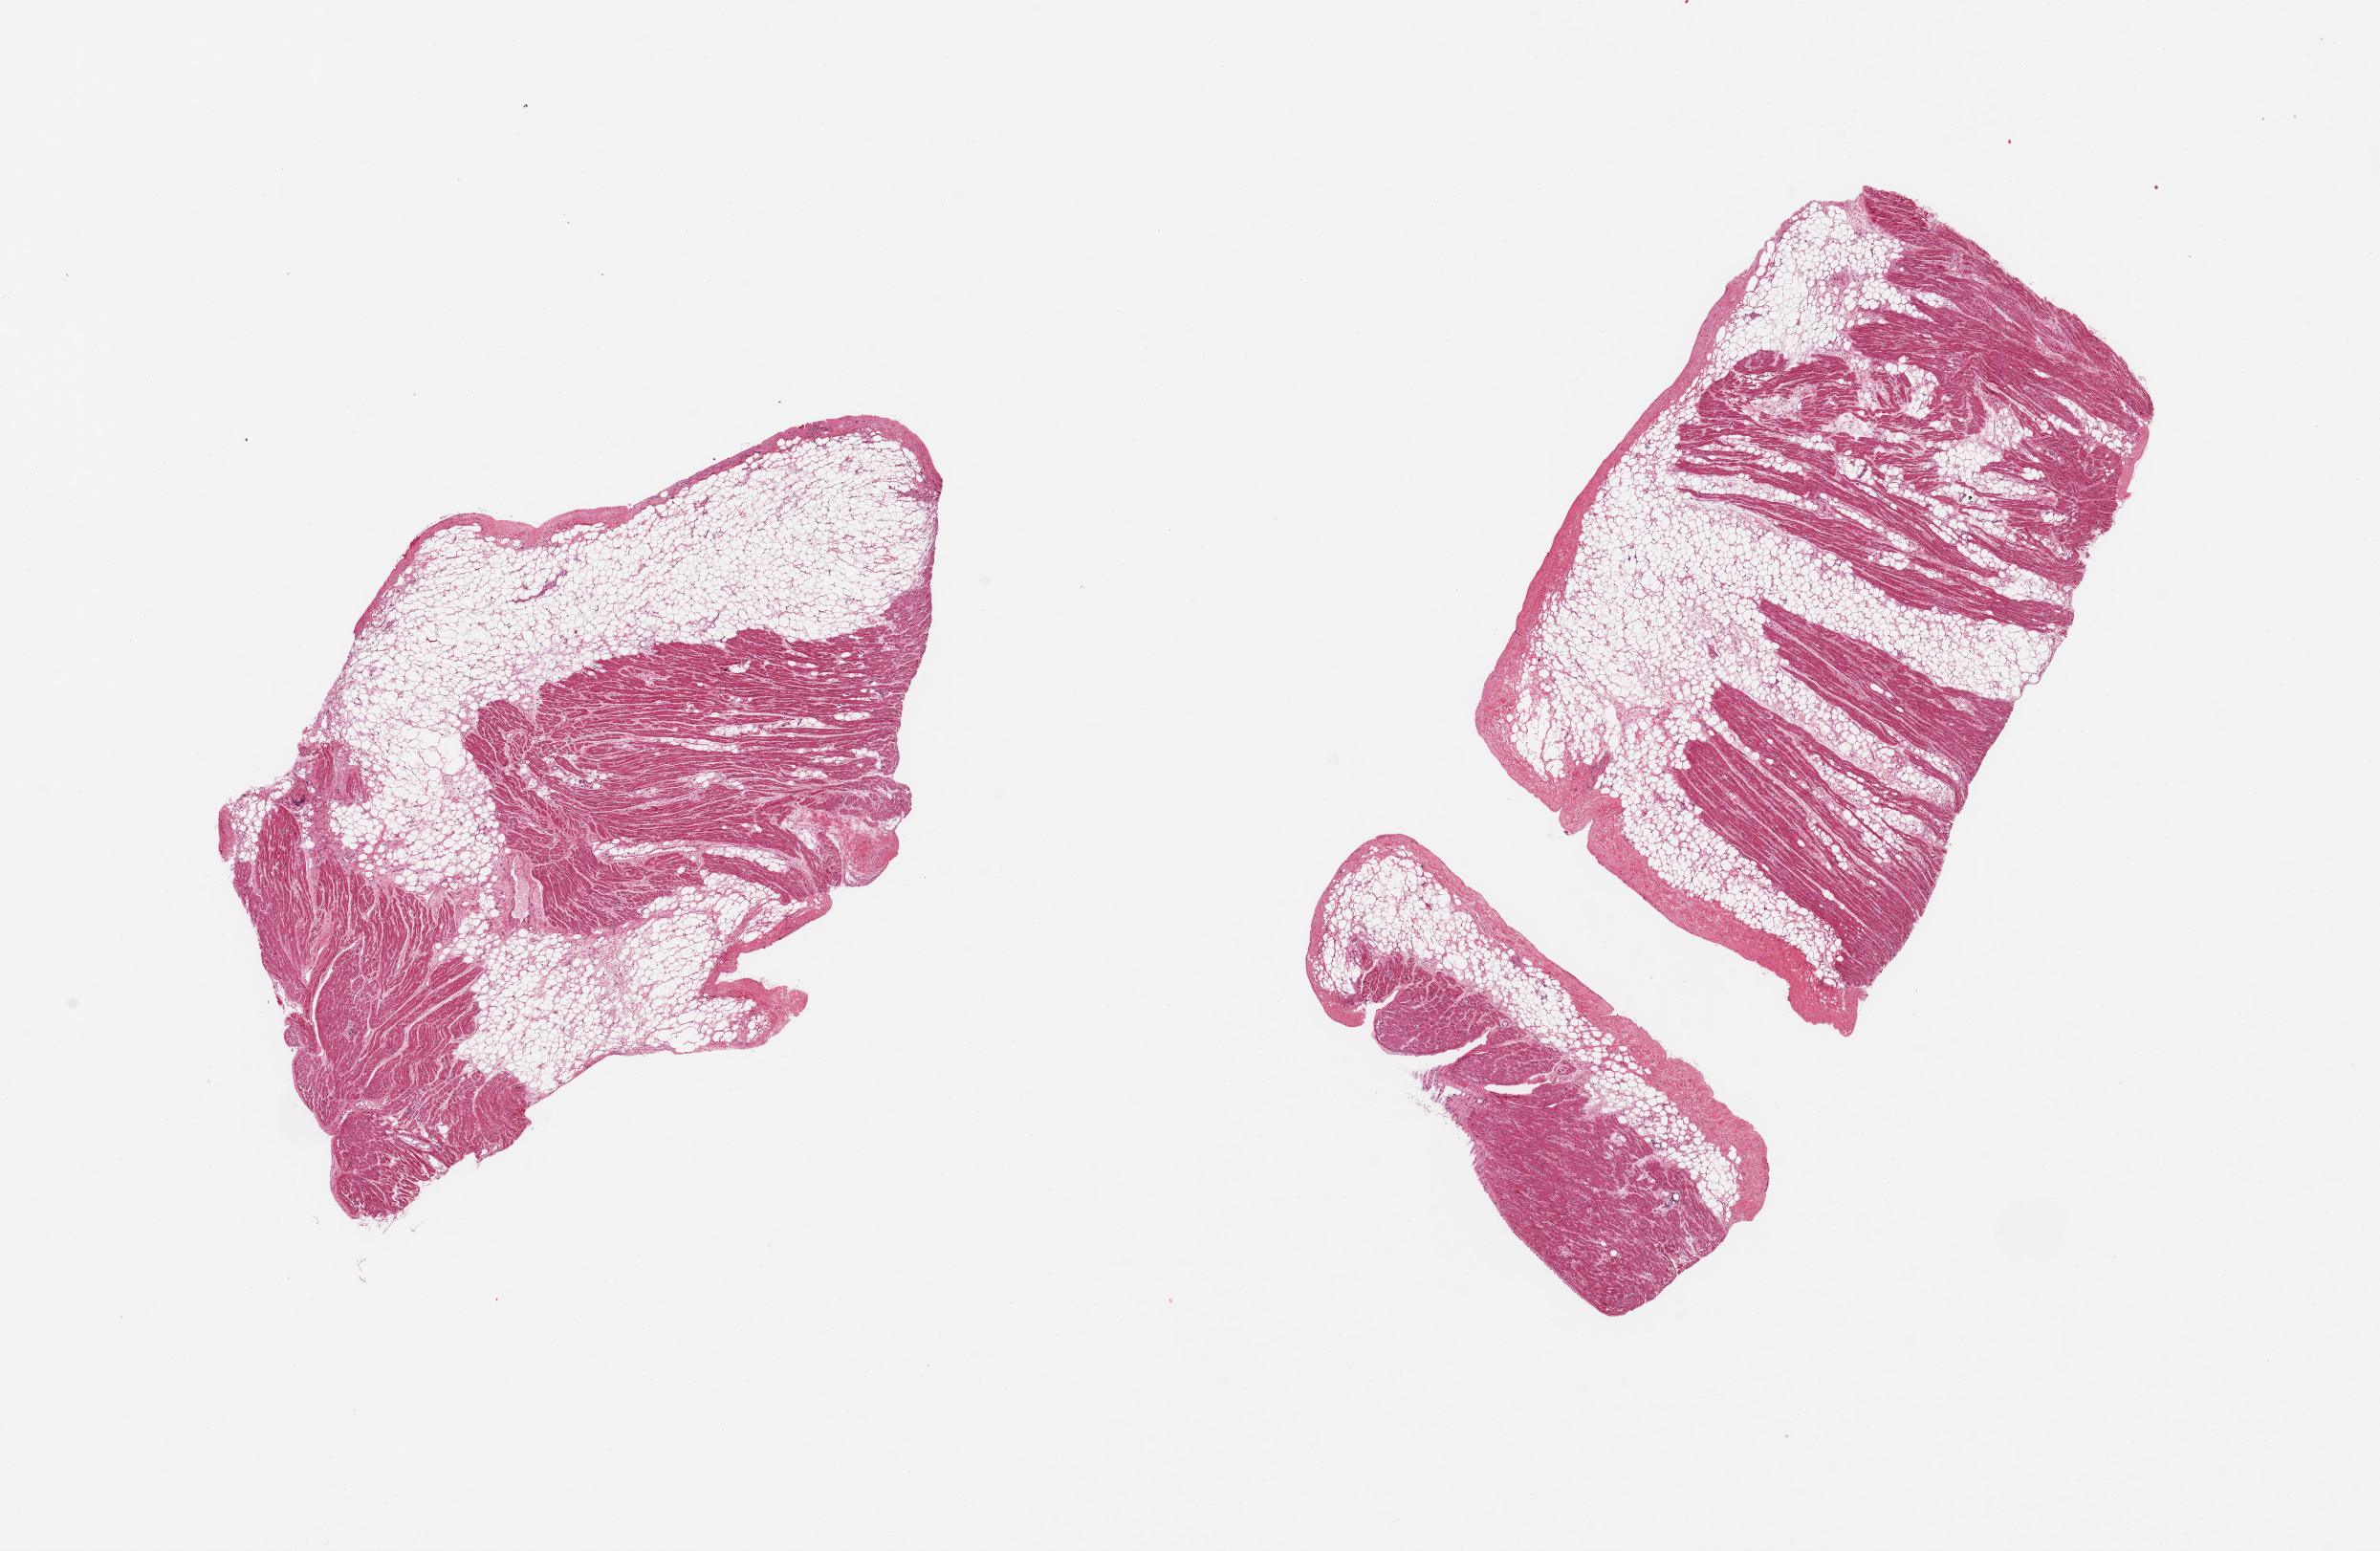
Whole-slide image, H&E stain, brightfield, a low-resolution overview of the entire scanned area, about 19.7 x 12.8 mm (slide scanned at 20x), PAXgene-fixed paraffin-embedded (PFPE) section, target tissue: auricular appendage, donor tissue sample. Male donor.
Pathologist's review note for this sample: 2 pieces; both are ~50% fat.